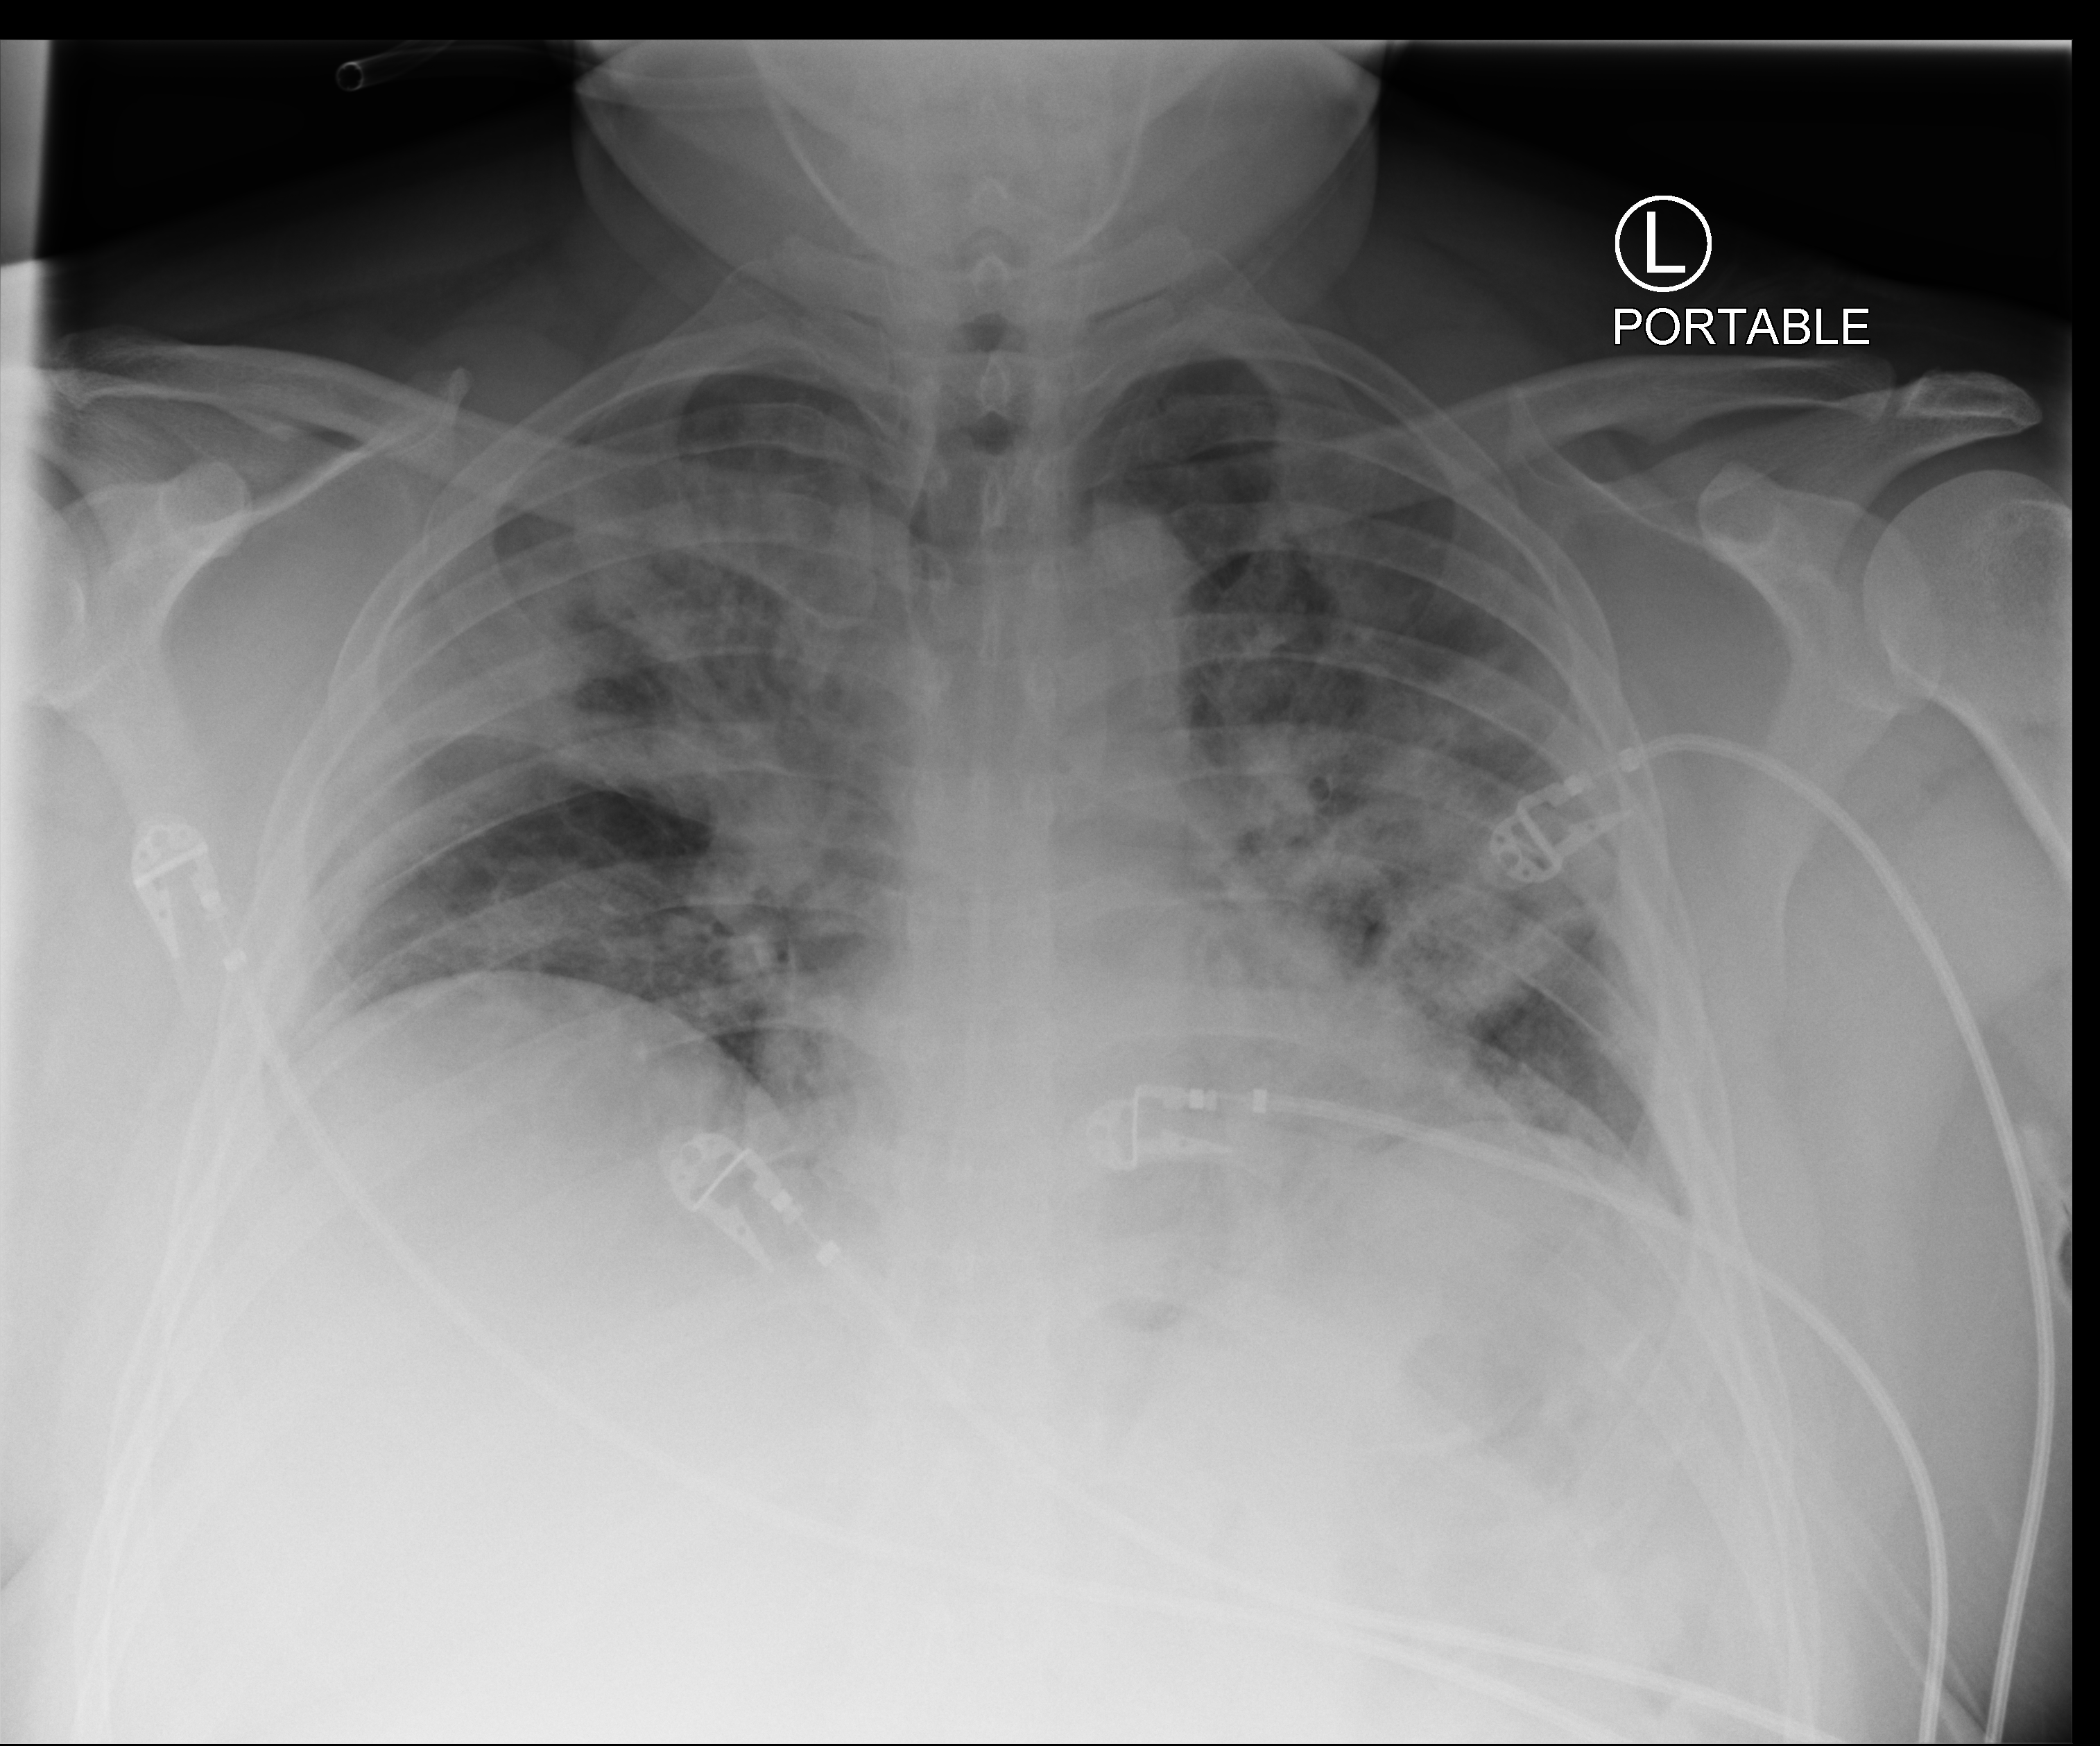
Portable chest radiograph. Male patient hospitalised with COVID-19, age 18–59 years.
Admission-level facts for this patient (not findings on this image; timing relative to this image not recorded):
- diabetes (admission record): no
- smoking status (admission record): never
- chronic kidney disease (admission record): no